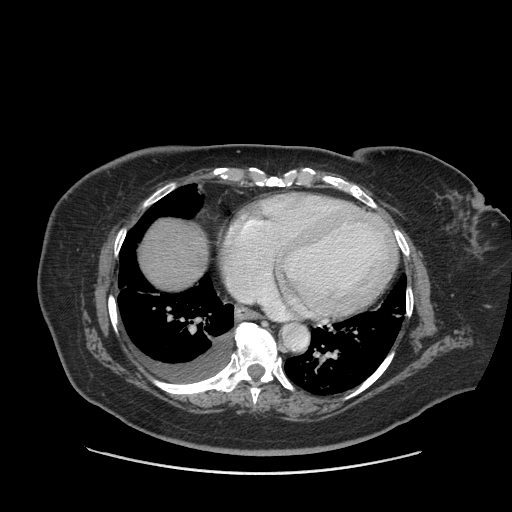
Contrast-enhanced abdominal CT (liver protocol), one axial slice. Position 84 of 91 along the scan axis. Soft-tissue window (W 400 / L 40 HU). 2.5 mm slice thickness. 512 × 512 image matrix, field of view 420 × 420 mm. Case-level facts recorded for this patient, not image findings: diagnosis: hepatocellular carcinoma (patient treated with transarterial chemoembolisation; whether this scan precedes or follows treatment is not stated here); TNM stage (as recorded): Stage-I; Child-Pugh class: A; tumour differentiation: well differentiated.
Annotated regions visible in this slice (semi-automatic segmentation, software-assisted and operator-edited):
- liver parenchyma outside the tumour (the mass and vessels are separate outlines, so this box may not span the whole liver): bounding box [x1, y1, x2, y2] px = [138, 216, 208, 288]